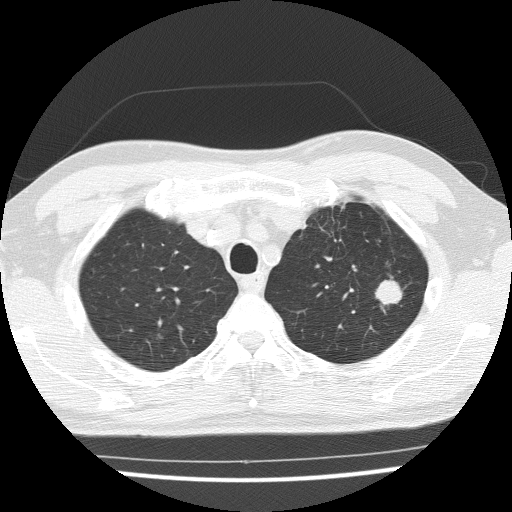
Low-dose screening chest CT, one axial slice. Position 121 of 154 along the scan axis. Lung window (W 1500 / L -600 HU). 2 mm slice thickness. 512 × 512 image matrix, field of view 330 × 330 mm.
Annotated regions visible in this slice (expert manual segmentation):
- lesion 1 (tumor, upper lobe of left lung): bounding box [x1, y1, x2, y2] px = [375, 280, 402, 305]